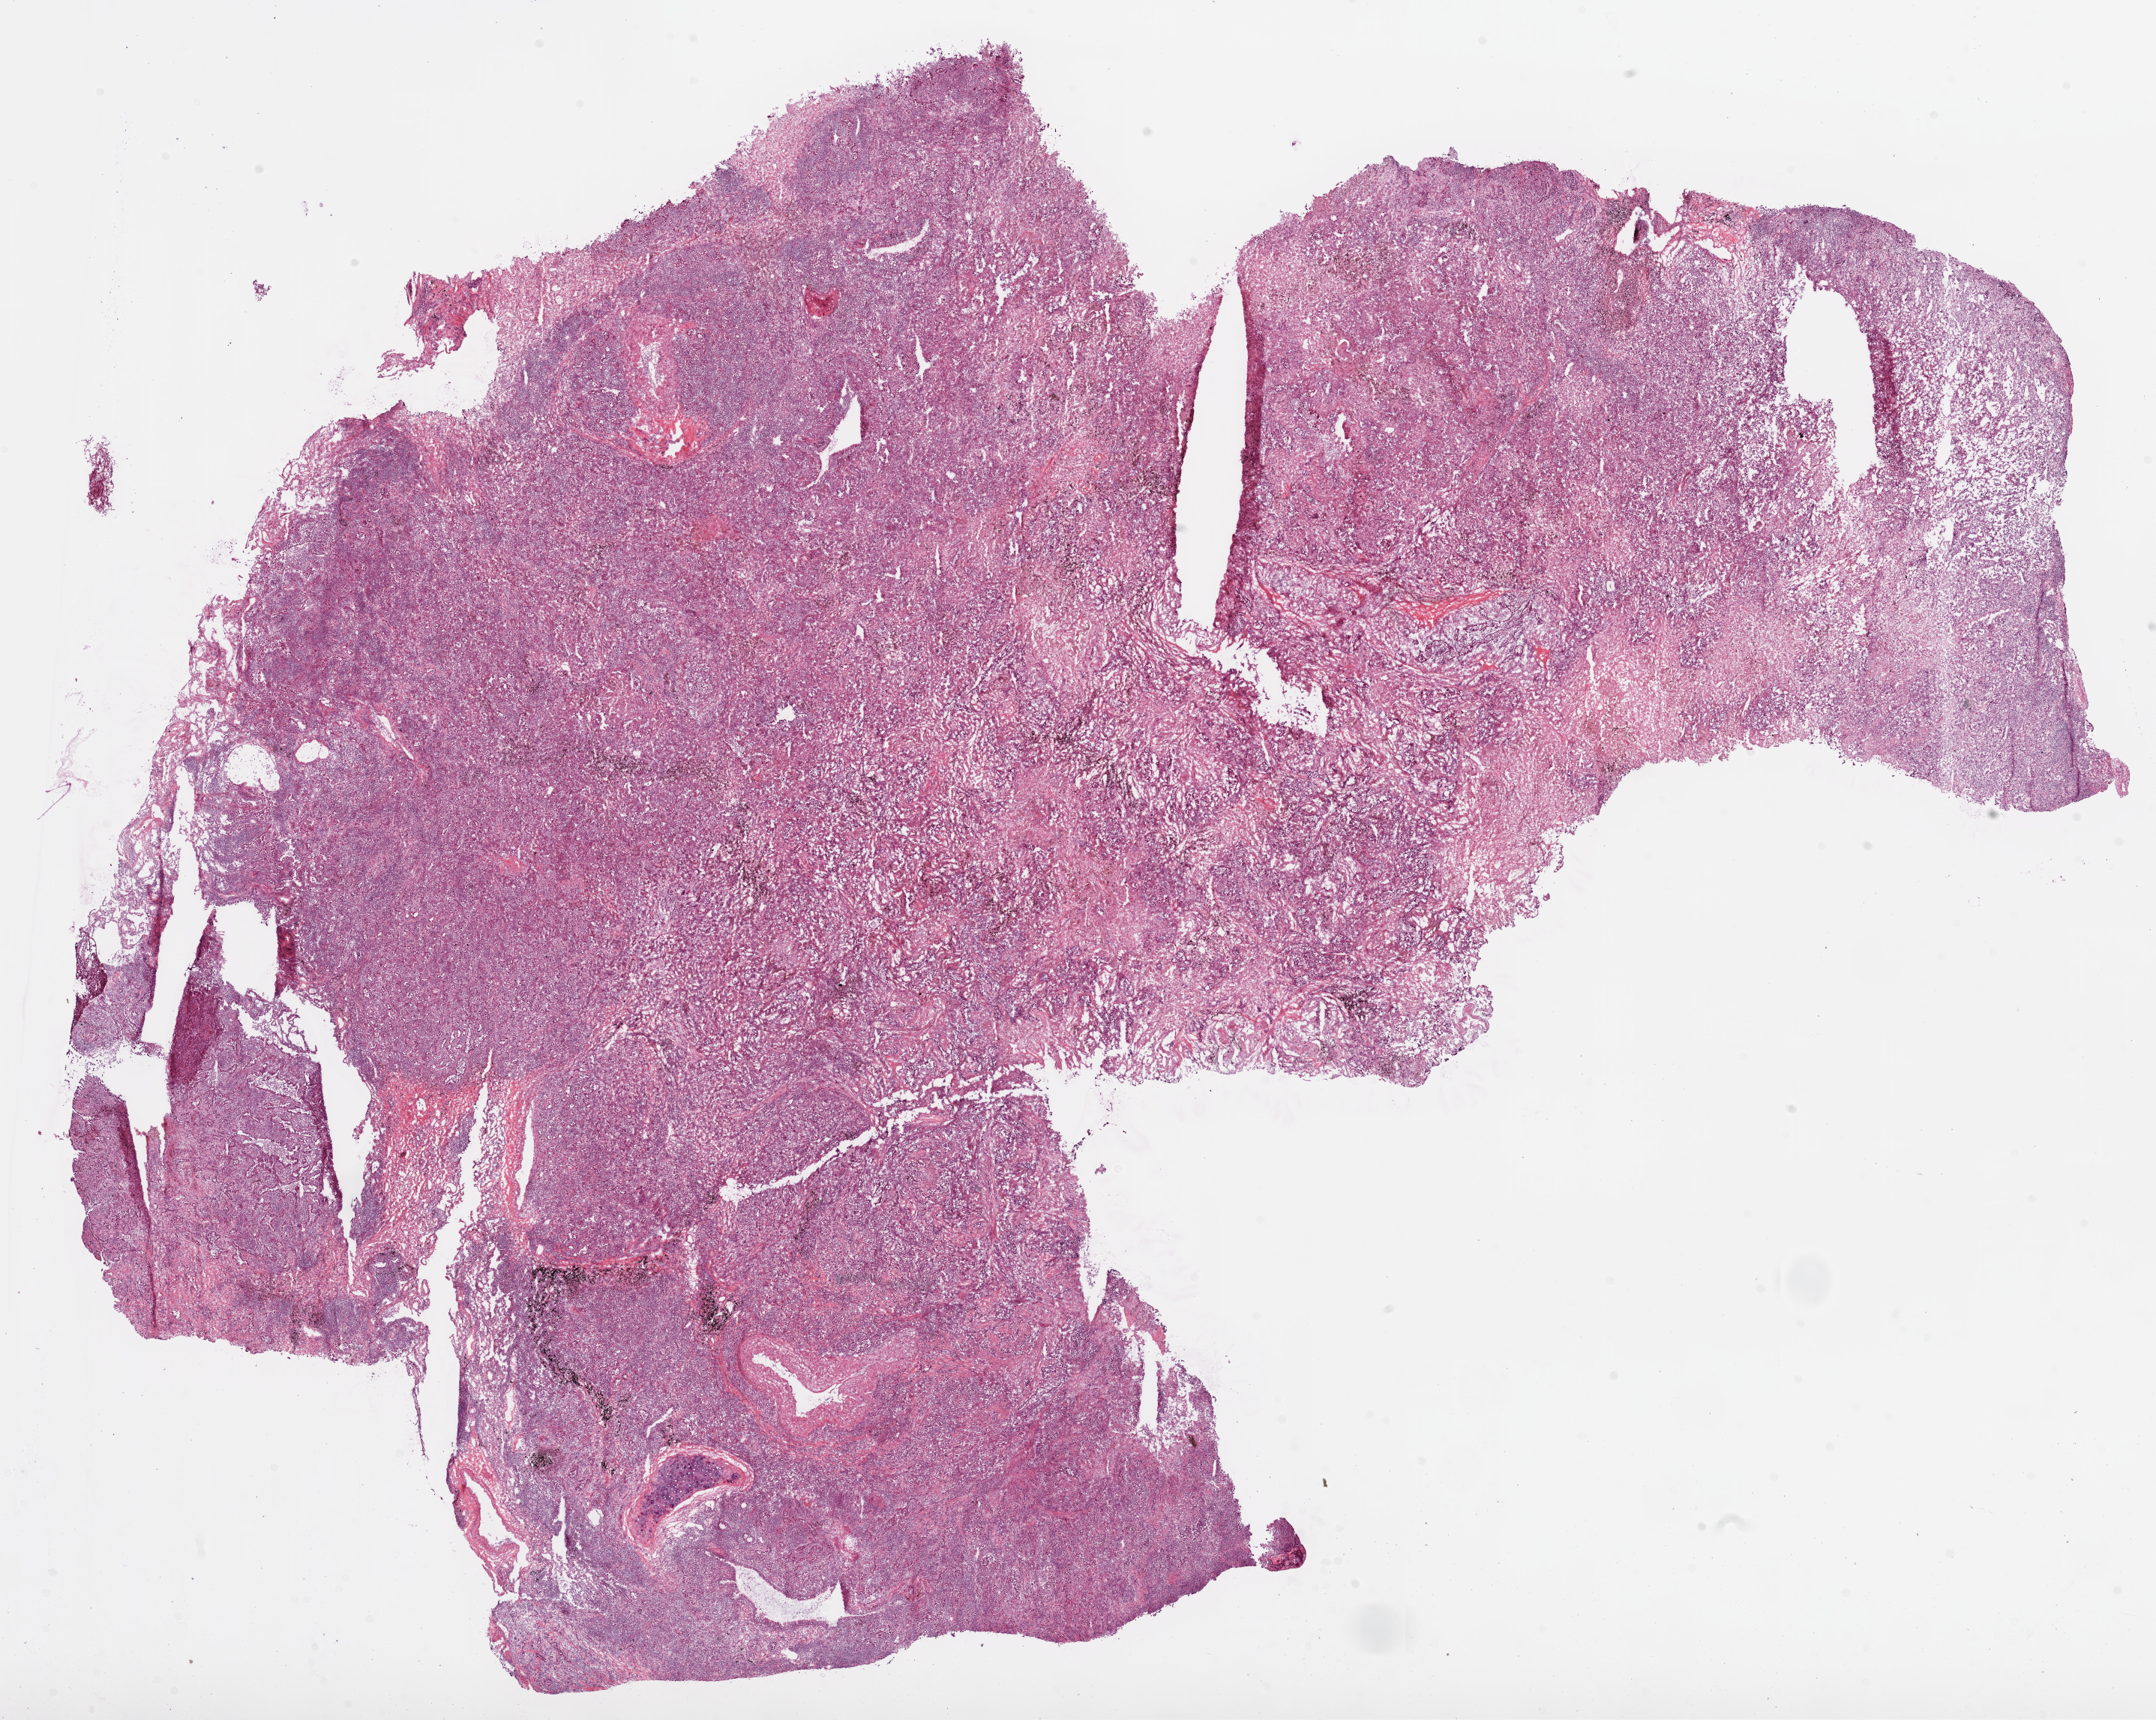
Whole-slide histology image, Hematoxylin and eosin (H&E) stained, shown as a low-resolution overview of the whole scanned area (about 23.1 x 18.4 mm). Frozen section. Lung, primary tumour sample. Patient: male, age at initial diagnosis 70 years. Composition of this section per pathologist review: tumour cells 57%, tumour nuclei 60%, normal cells 10%, stromal cells 30%, necrosis 3%.
- diagnosis: Adenocarcinoma, NOS (upper lobe, lung)
- TNM: T2 N0 M0
- AJCC pathologic stage: IA (6th edition)